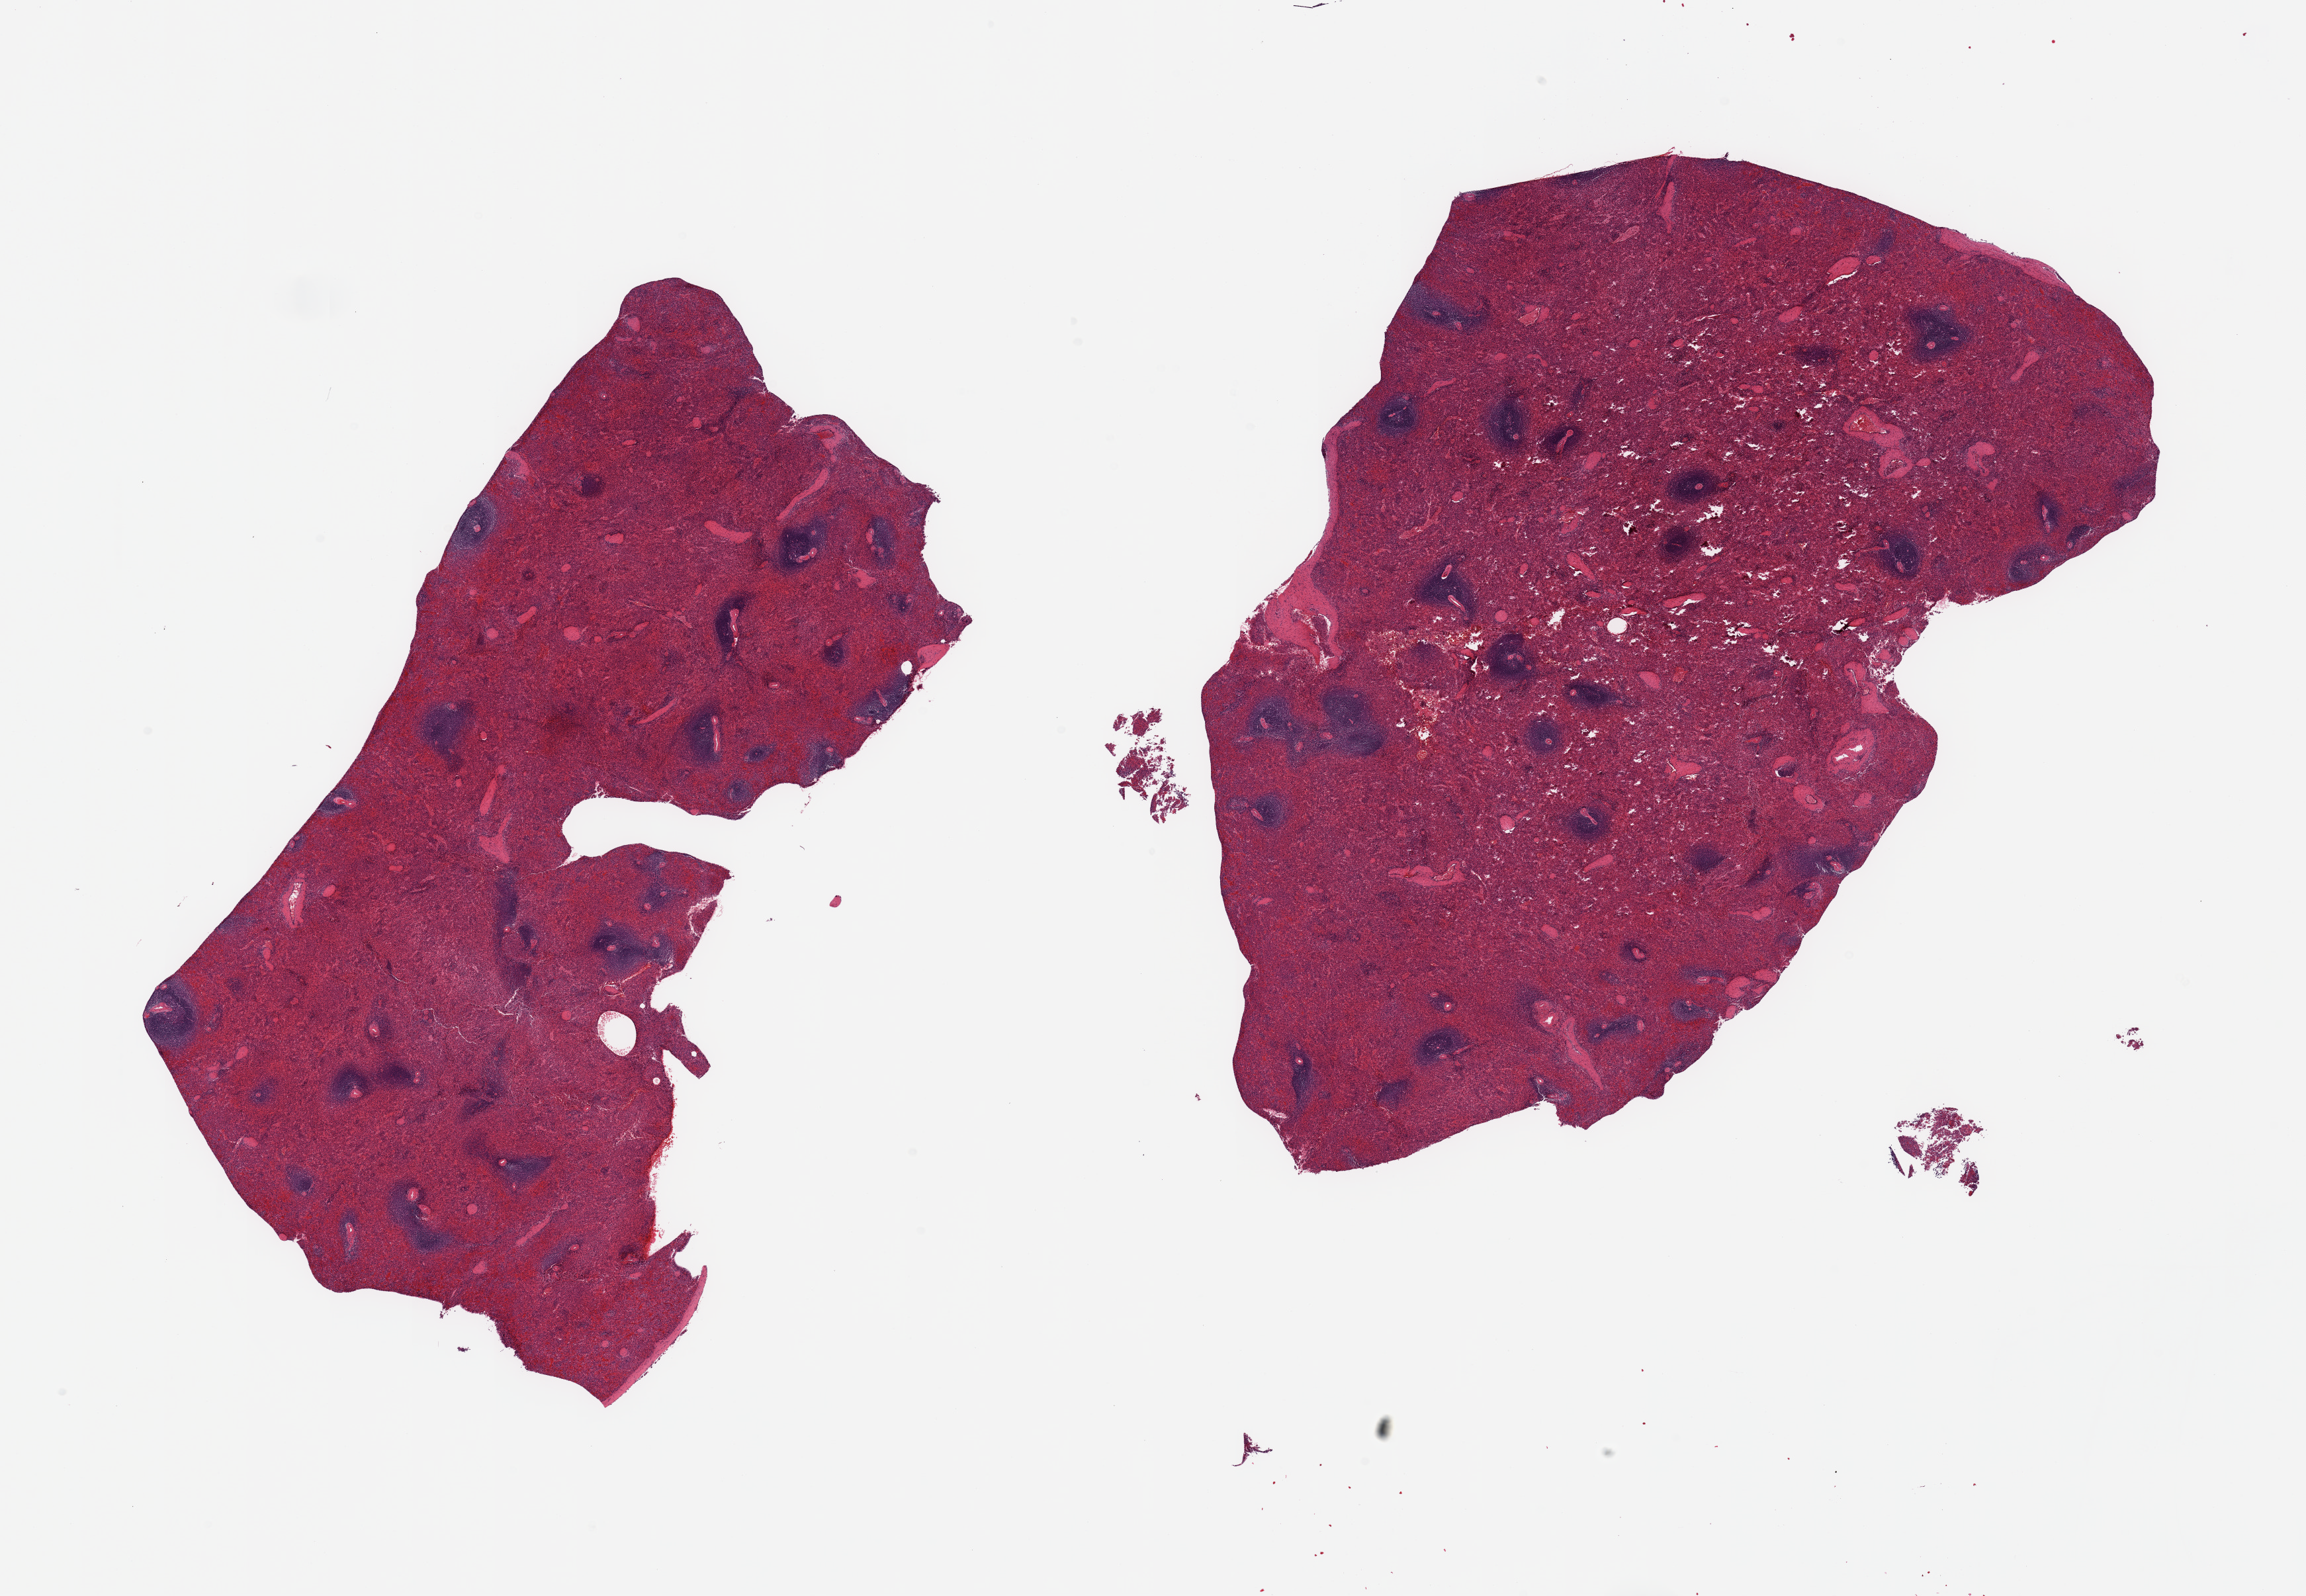
Hematoxylin and eosin (H&E) whole-slide image, a low-resolution overview of the entire scanned area, about 27.6 x 19.1 mm (acquisition: 20x scan); PAXgene-fixed paraffin-embedded (PFPE) section; target tissue: spleen; tissue donor sample.
Pathologist's review note for this sample: 2 pieces, no abnormalities.